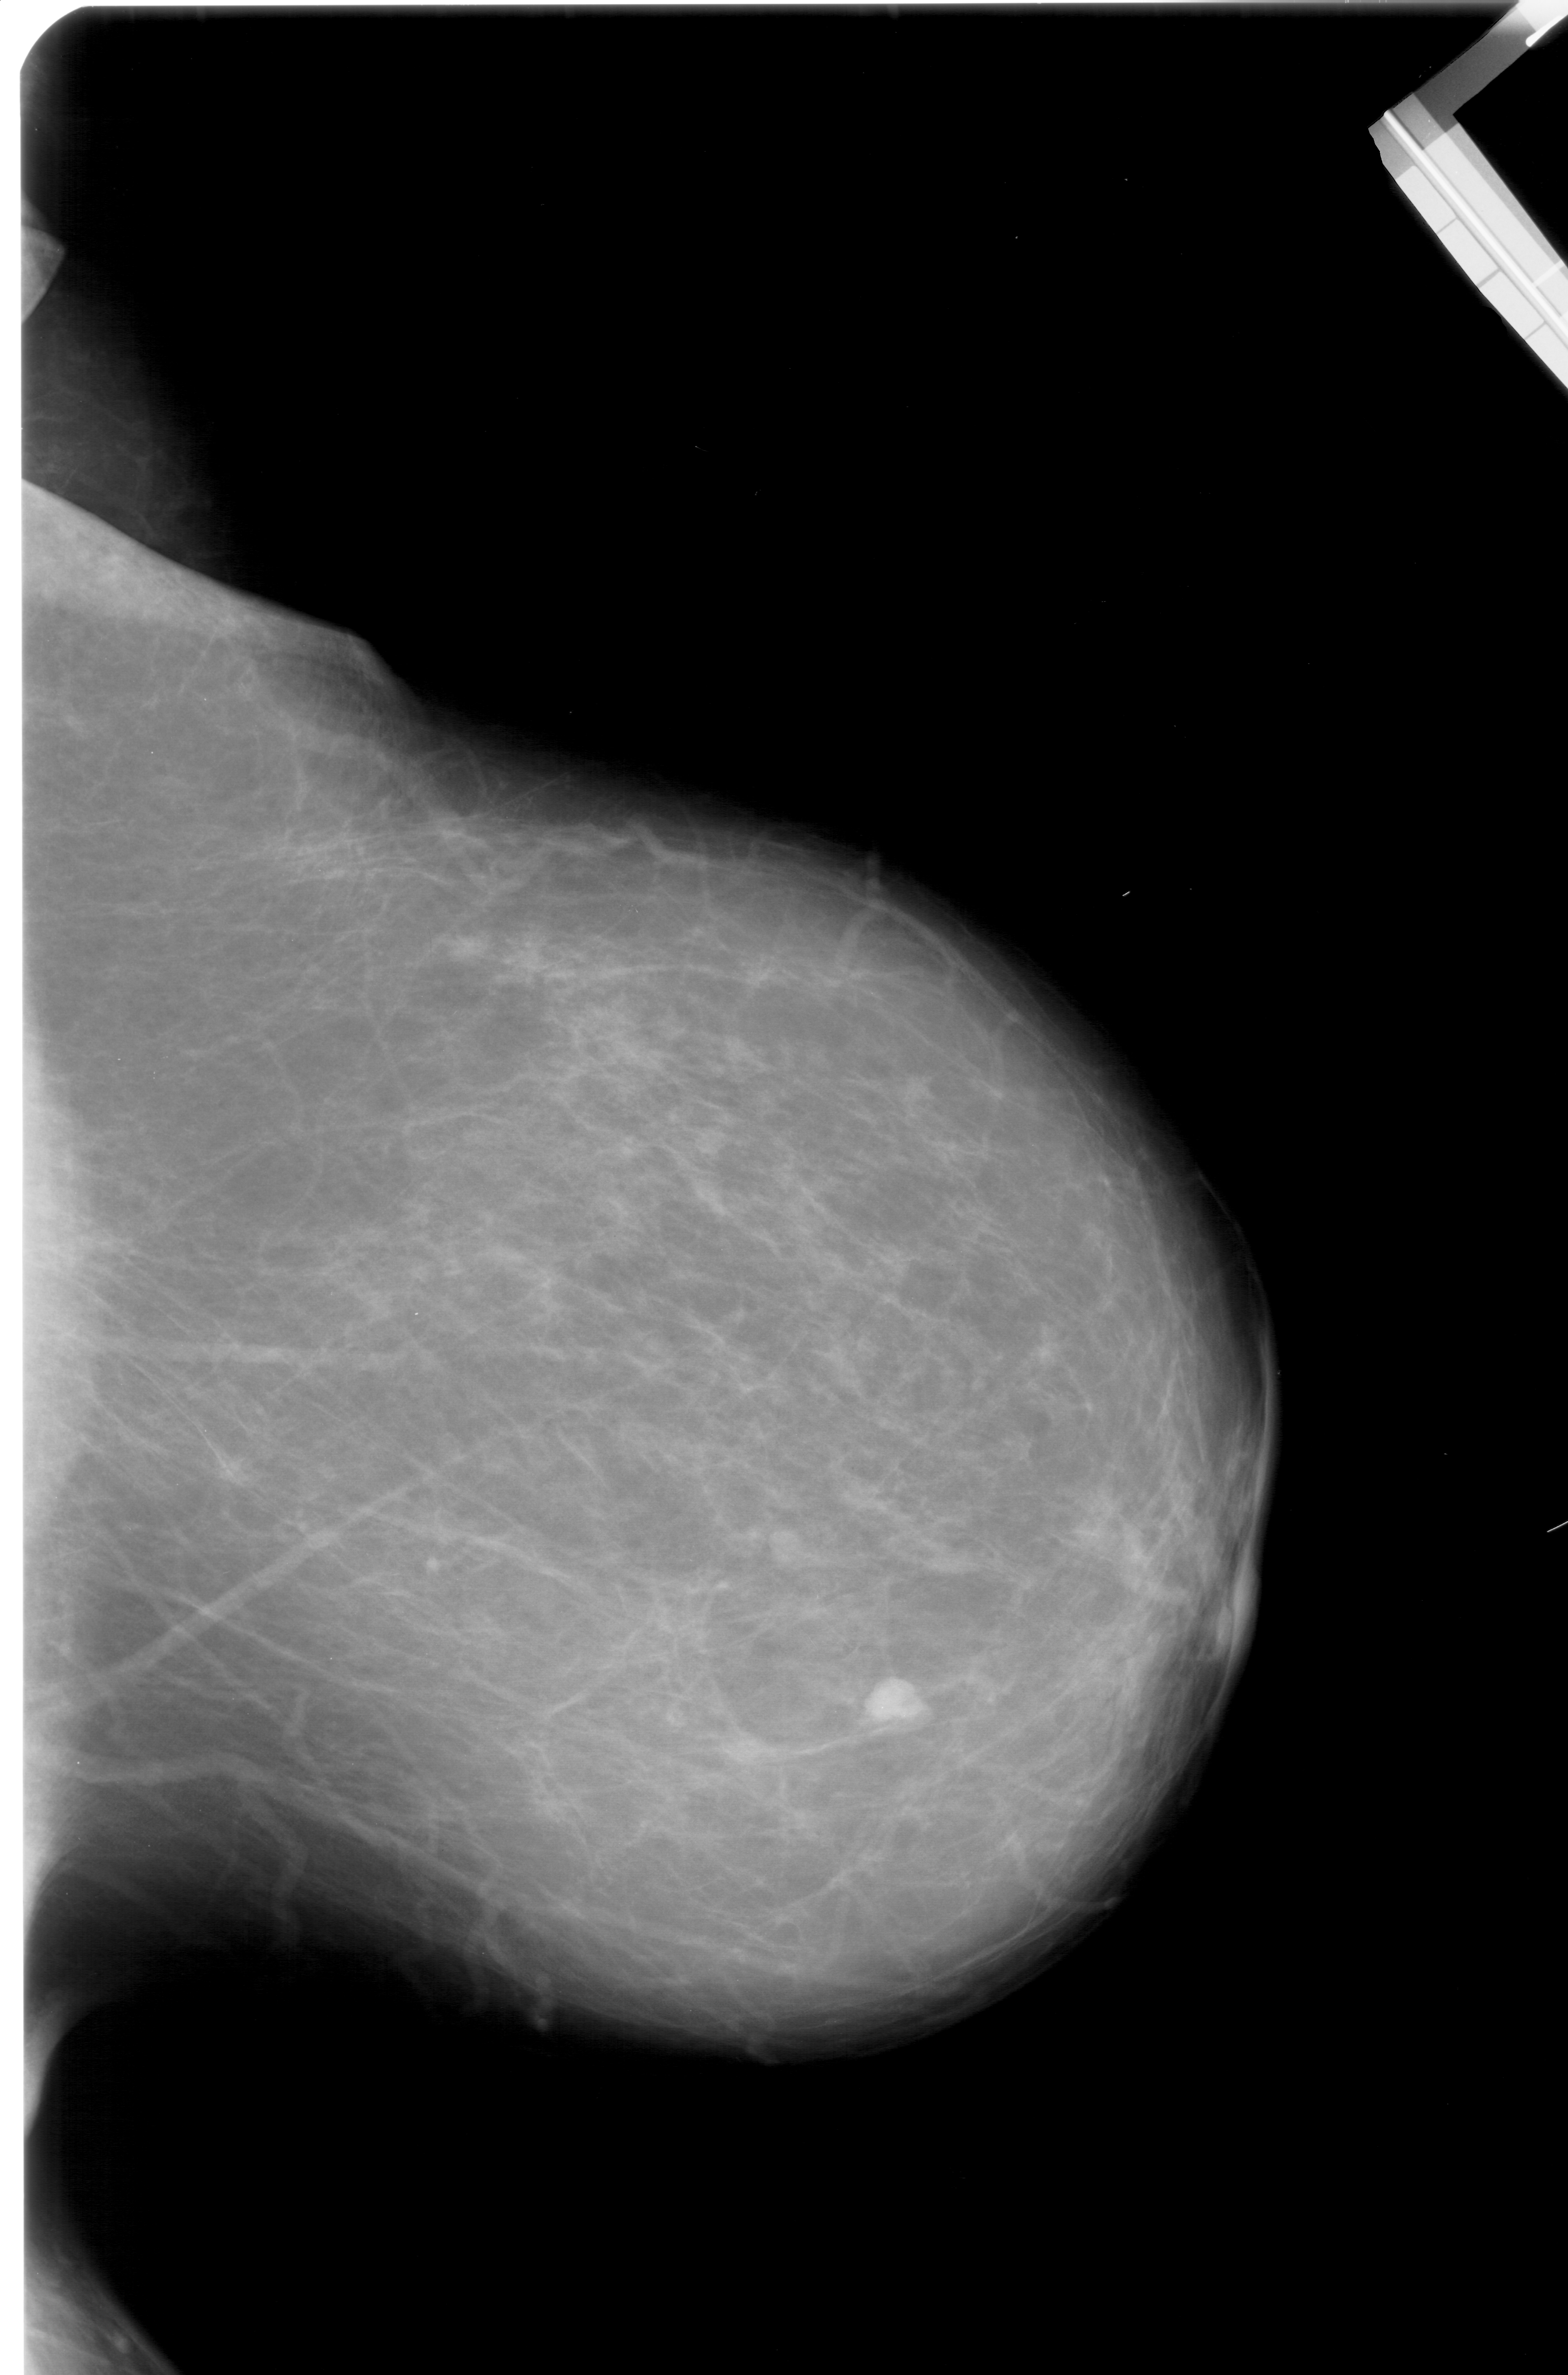
Mammogram (digitized film); right breast; CC view; BI-RADS breast density category 2 (scale 1–4); 1568 × 2375 image matrix.
Expert-marked regions of interest on this film, with their recorded descriptors:
- mass, shape lobulated, margins circumscribed; BI-RADS assessment category 4; pathology result (as recorded, not read from the image): malignant: bounding box [x1, y1, x2, y2] px = [853, 1669, 936, 1740]